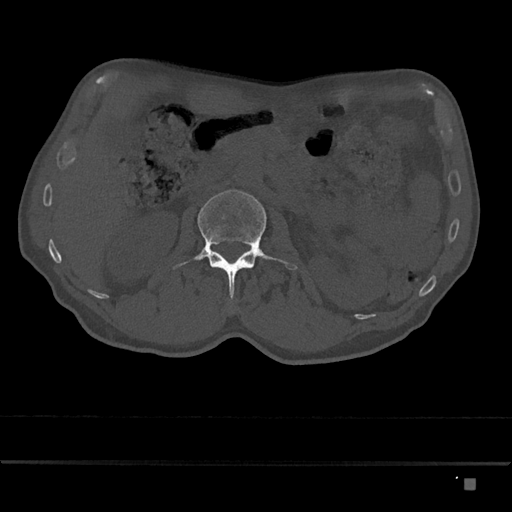
CT including the spine, one axial slice. Slice 476 of 797 in the series (ordered by position). Reconstruction kernel Br40s/3. Bone window (W 1800 / L 400 HU). 0.5 mm slice thickness. 512 × 512 image matrix. Patient: male, 72 years. Case-level facts recorded for this patient, not image findings: primary cancer: prostate.
Structures marked on this image (semi-automatically segmented with operator editing):
- L2 vertebra: bounding box <173,189,297,302> (left, top, right, bottom; pixels)